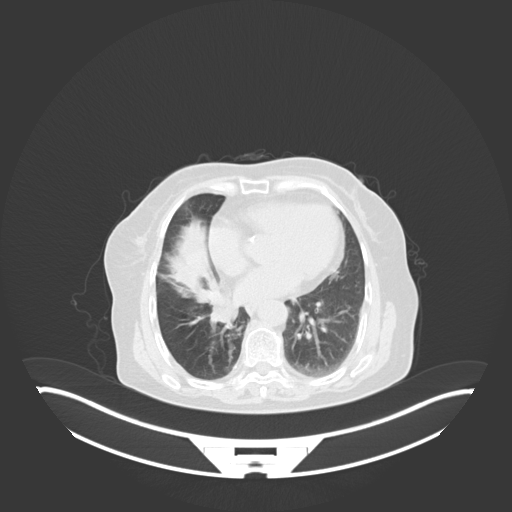
Chest CT, one axial slice; slice 19 of 76 in the series (ordered by position); 120 kVp; lung window (W 1500 / L -600 HU); 3 mm slice thickness; 512 × 512 image matrix, field of view 500 × 500 mm. Patient: female, 75 years. Case-level facts recorded for this patient, not image findings: clinical TNM (as recorded): T1b N0 M1a.
Structures marked on this image (bounding box drawn by a radiologist):
- lung tumour (recorded histology: squamous cell carcinoma): box from (x=212, y=297) to (x=241, y=325) px